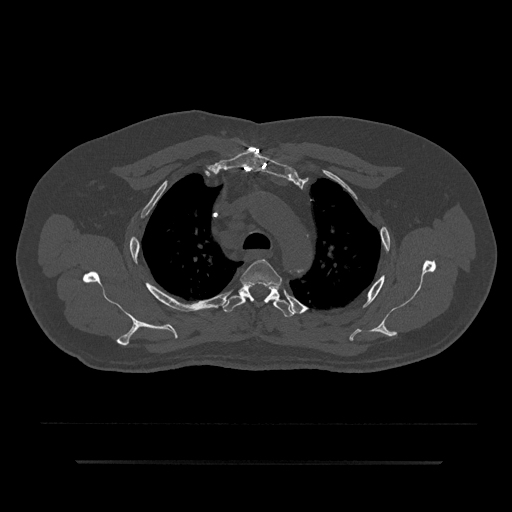
CT including the spine, one axial slice; position 636 of 797 along the scan axis; bone window (W 1800 / L 400 HU); 512 × 512 image matrix, field of view 464 × 464 mm. Patient: male, 59 years. From the clinical record (not read from this slice): primary cancer: bile ducts; vertebrae with lytic lesions (as recorded): T10.
Structures marked on this image (semi-automatically segmented with operator editing):
- T3 vertebra: bounding box <240,259,282,288> (left, top, right, bottom; pixels)
- T4 vertebra: <222,283,294,317>